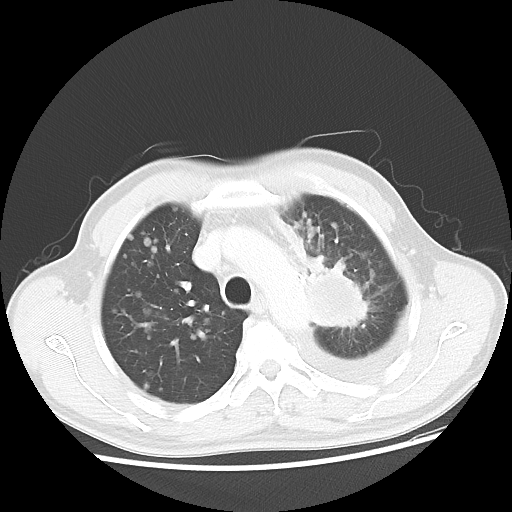
Chest CT, one axial slice; reconstruction kernel LUNG; 100 kVp; lung window (W 1500 / L -600 HU); 5 mm slice thickness; 512 × 512 image matrix. Patient: male, 55 years. Case-level facts recorded for this patient, not image findings: clinical TNM (as recorded): T2 N3 M1a; histopathological grade: G3.
Outlined on this slice (rectangle marked by the reading radiologist):
- lung tumour (recorded histology: squamous cell carcinoma): box from (x=315, y=245) to (x=372, y=339) px